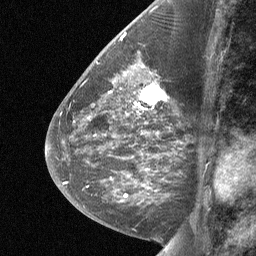
Breast MRI (dynamic contrast-enhanced), one sagittal slice; position 29 of 64 along the scan axis; dynamic contrast-enhanced study with each time point stored as its own series, time point 2 of 3 at this slice position (early post-contrast, ordered by acquisition time); 1.5 T; TE 4.8 ms, TR 27 ms; 2 mm slice thickness; 256 × 256 image matrix, field of view 180 × 180 mm. Patient: female, 59 years. From the clinical record (not read from this slice): setting: breast cancer imaged before/during neoadjuvant chemotherapy; receptor status: triple-negative.
Structures marked on this image (semi-automatically segmented with operator editing):
- analysis volume of interest (the breast-tissue region the enhancement analysis was run in; not a lesion): bounding box <126,75,173,114> (left, top, right, bottom; pixels)
- tumour enhancement mask (voxels above the 90 % enhancement threshold inside the analysis volume of interest): <134,82,166,109>